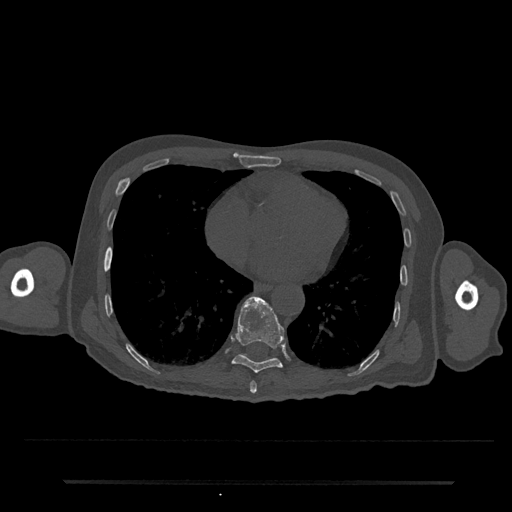
CT including the spine, one axial slice. Position 361 of 797 along the scan axis. Reconstruction kernel Br40s/3. 120 kVp. Bone window (W 1800 / L 400 HU). 512 × 512 image matrix, field of view 427 × 427 mm. Patient: male, 74 years. Case-level facts recorded for this patient, not image findings: primary cancer: prostate.
Structures marked on this image (semi-automatically segmented with operator editing):
- T8 vertebra: box from (x=250, y=381) to (x=257, y=394) px
- T9 vertebra: (x=232, y=296)–(x=285, y=373)